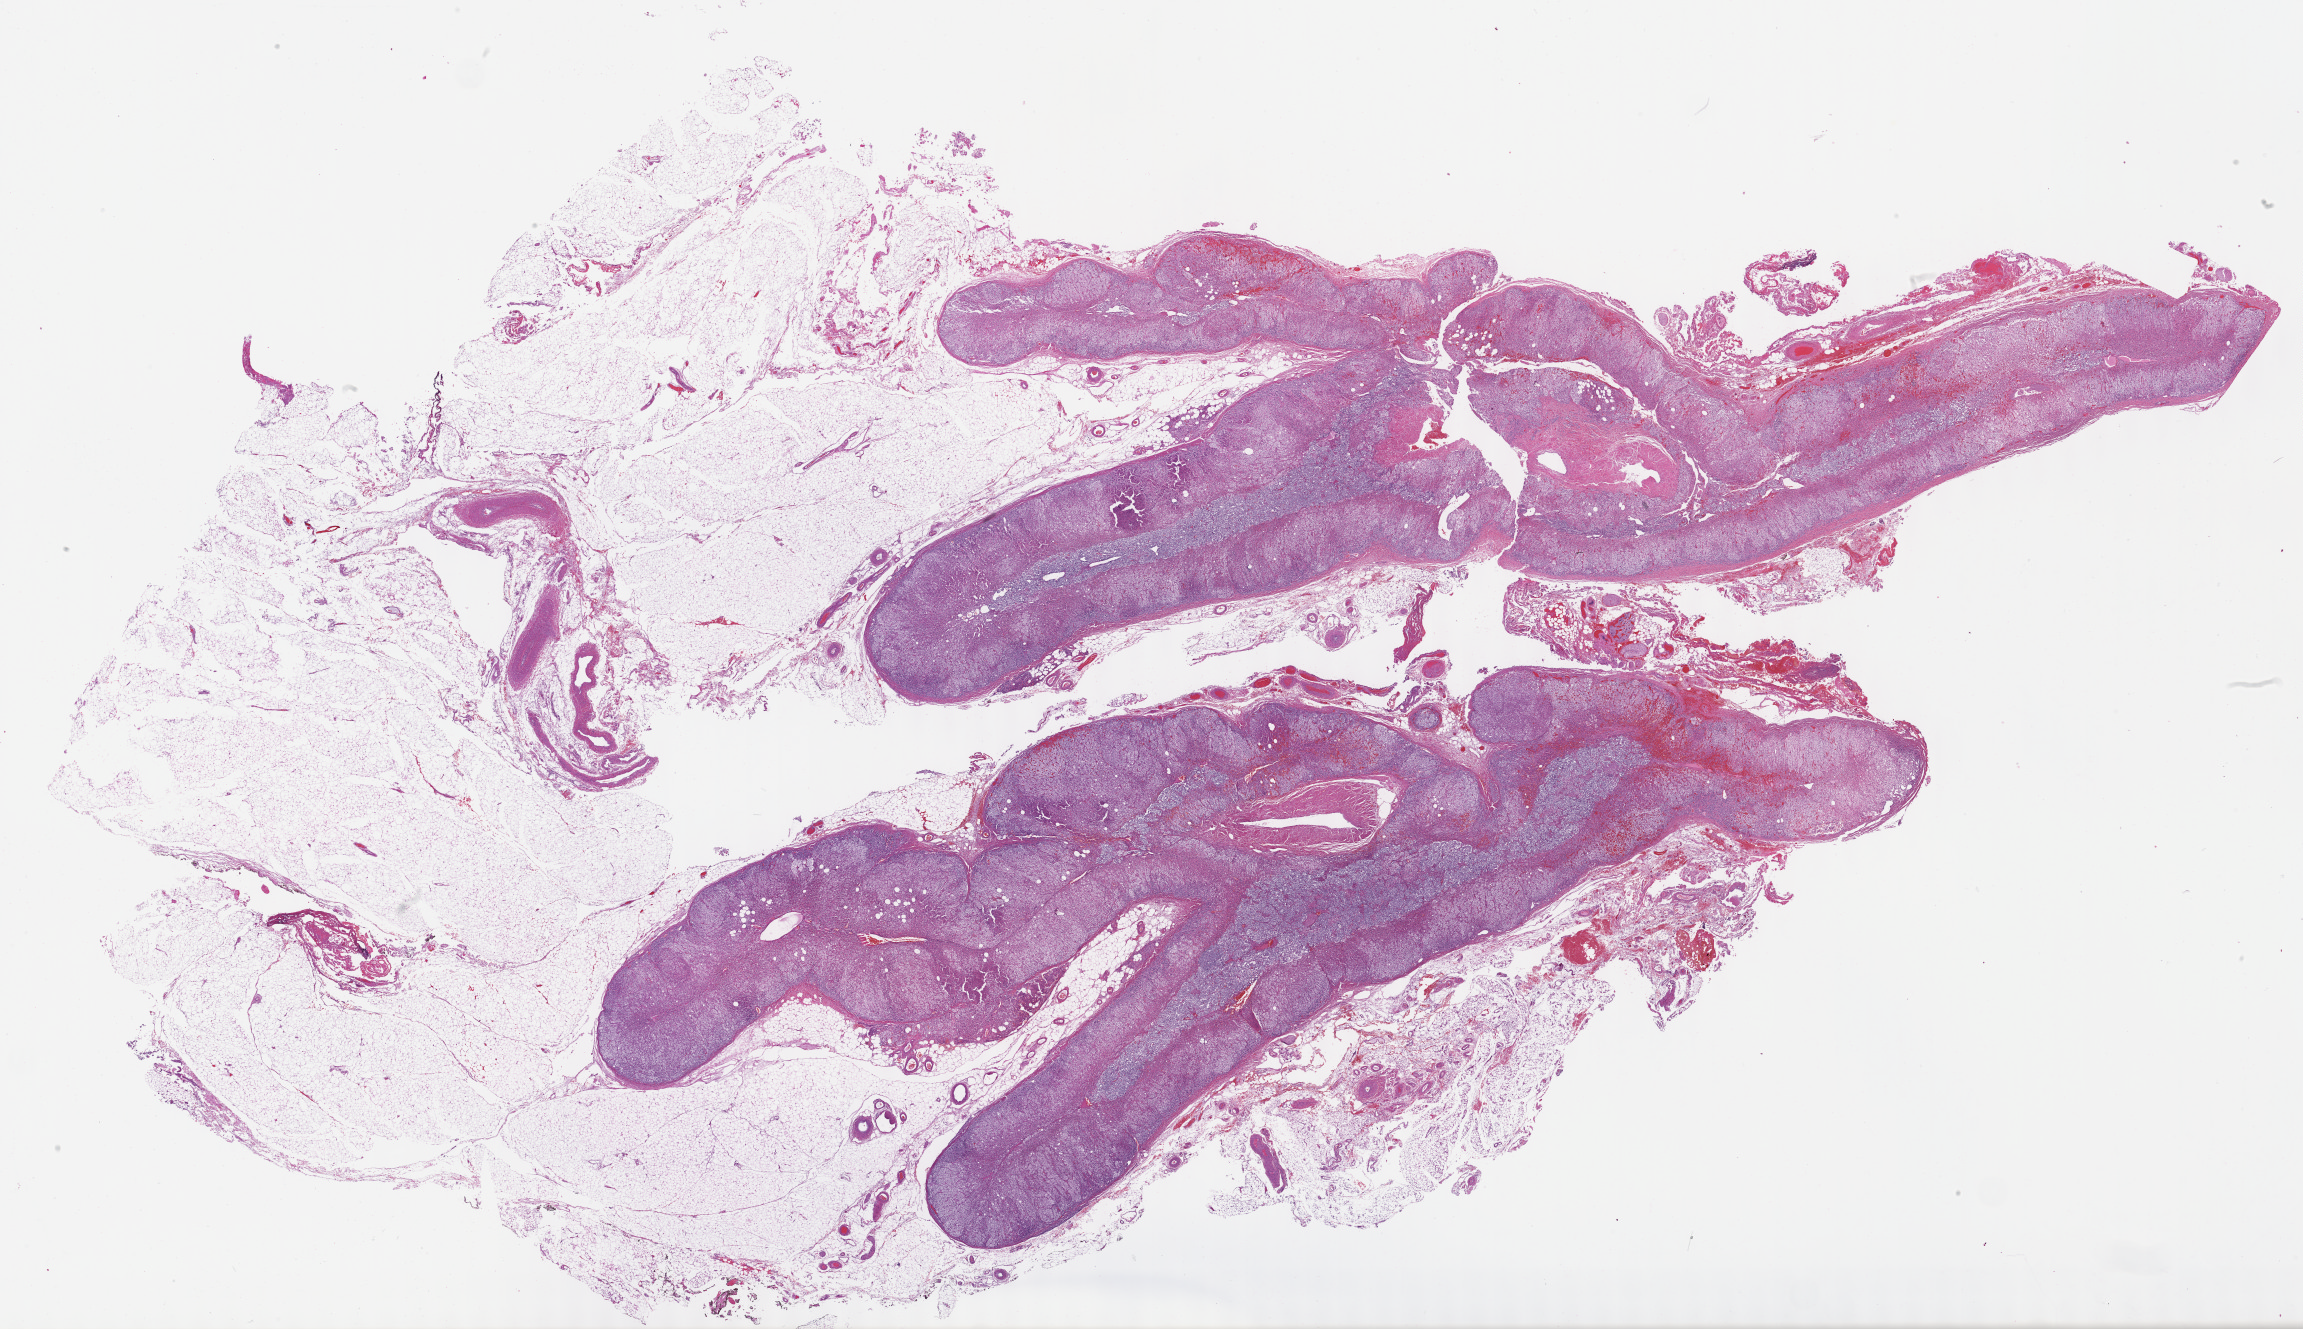
Digitized H&E-stained tissue section (whole slide) — low-resolution overview of the scanned area, about 37.2 x 21.5 mm (slide scanned at 40x), FFPE section, sample: primary tumour, adrenal gland. Female patient; age at initial diagnosis 52 years.
Histologic diagnosis: Pheochromocytoma, NOS.